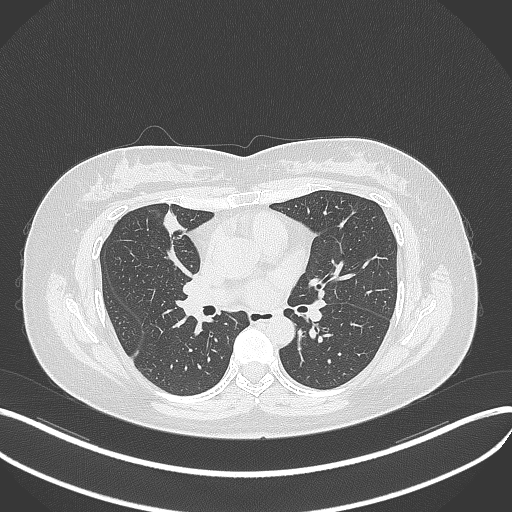
Chest CT, one axial slice; position 167 of 273 along the scan axis; reconstruction kernel B70f; 120 kVp; lung window (W 1500 / L -600 HU); 1 mm slice thickness; 512 × 512 image matrix, field of view 400 × 400 mm. Patient: female, 42 years. Case-level facts recorded for this patient, not image findings: clinical TNM (as recorded): T1b N0 M0.
Annotated regions visible in this slice (rectangle marked by the reading radiologist):
- lung tumour (recorded histology: adenocarcinoma): box from (x=155, y=204) to (x=189, y=244) px